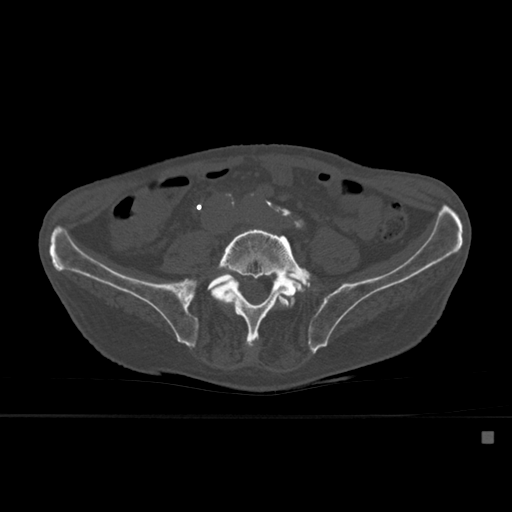
CT including the spine, one axial slice. Position 177 of 527 along the scan axis. Bone window (W 1800 / L 400 HU). 1.5 mm slice thickness. 512 × 512 image matrix. Male patient, age 78 years. Case-level facts recorded for this patient, not image findings: primary cancer: prostate.
Annotated regions visible in this slice (semi-automatically segmented with operator editing):
- L4 vertebra: bounding box <222,294,294,310> (left, top, right, bottom; pixels)
- L5 vertebra: <212,227,312,349>